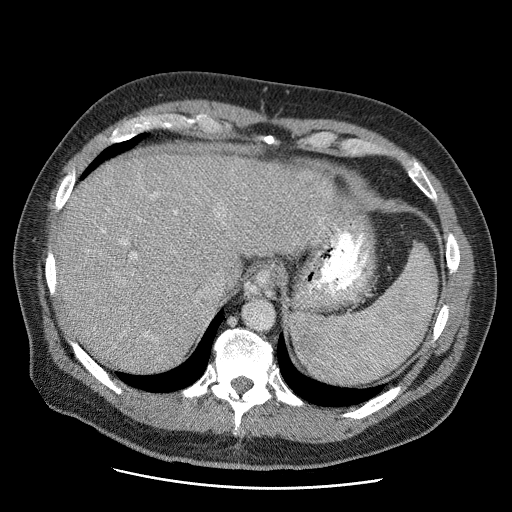
Contrast-enhanced abdominal CT (liver protocol), one axial slice. Slice 45 of 81 in the series (ordered by position). 120 kVp. Soft-tissue window (W 400 / L 40 HU). 2.5 mm slice thickness. 512 × 512 image matrix, field of view 380 × 380 mm. From the clinical record (not read from this slice): diagnosis: hepatocellular carcinoma (patient treated with transarterial chemoembolisation; whether this scan precedes or follows treatment is not stated here); TNM stage (as recorded): Stage-IIIA; Child-Pugh class: A; tumour differentiation: moderately differentiated; tumour nodularity: multinodular.
Annotated regions visible in this slice (semi-automatic segmentation, software-assisted and operator-edited):
- liver parenchyma outside the tumour (the mass and vessels are separate outlines, so this box may not span the whole liver): bounding box [x1, y1, x2, y2] px = [56, 149, 353, 370]
- liver vessels: [102, 211, 225, 336]